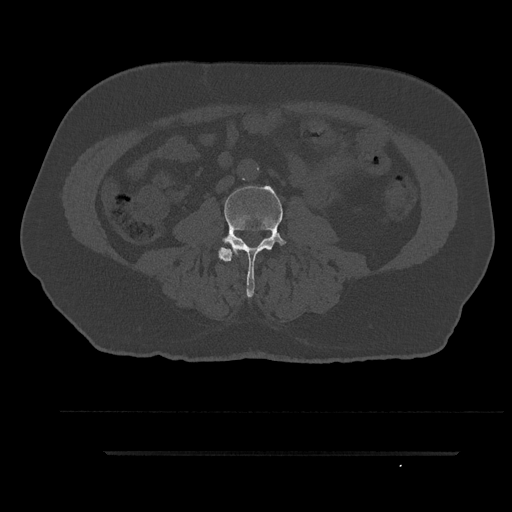
CT including the spine, one axial slice. Position 36 of 797 along the scan axis. 120 kVp. Bone window (W 1800 / L 400 HU). 0.5 mm slice thickness. 512 × 512 image matrix, field of view 432 × 432 mm. Patient: male, 63 years. Case-level facts recorded for this patient, not image findings: primary cancer: renal; vertebrae with lytic lesions (as recorded): T8.
Annotated regions visible in this slice (semi-automatic segmentation, software-assisted and operator-edited):
- L3 vertebra: box from (x=218, y=185) to (x=286, y=298) px